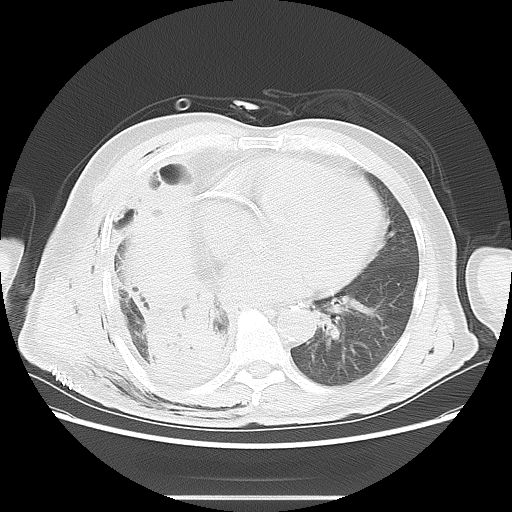
Chest CT, one axial slice. Position 27 of 59 along the scan axis. Reconstruction kernel LUNG. 120 kVp. Lung window (W 1500 / L -600 HU). 5 mm slice thickness. 512 × 512 image matrix. Patient: male, 69 years. Case-level facts recorded for this patient, not image findings: clinical TNM (as recorded): T3 N0 M0; histopathological grade: G2-3.
Structures marked on this image (bounding box drawn by a radiologist):
- lung tumour (recorded histology: squamous cell carcinoma): bounding box [x1, y1, x2, y2] px = [142, 306, 241, 398]